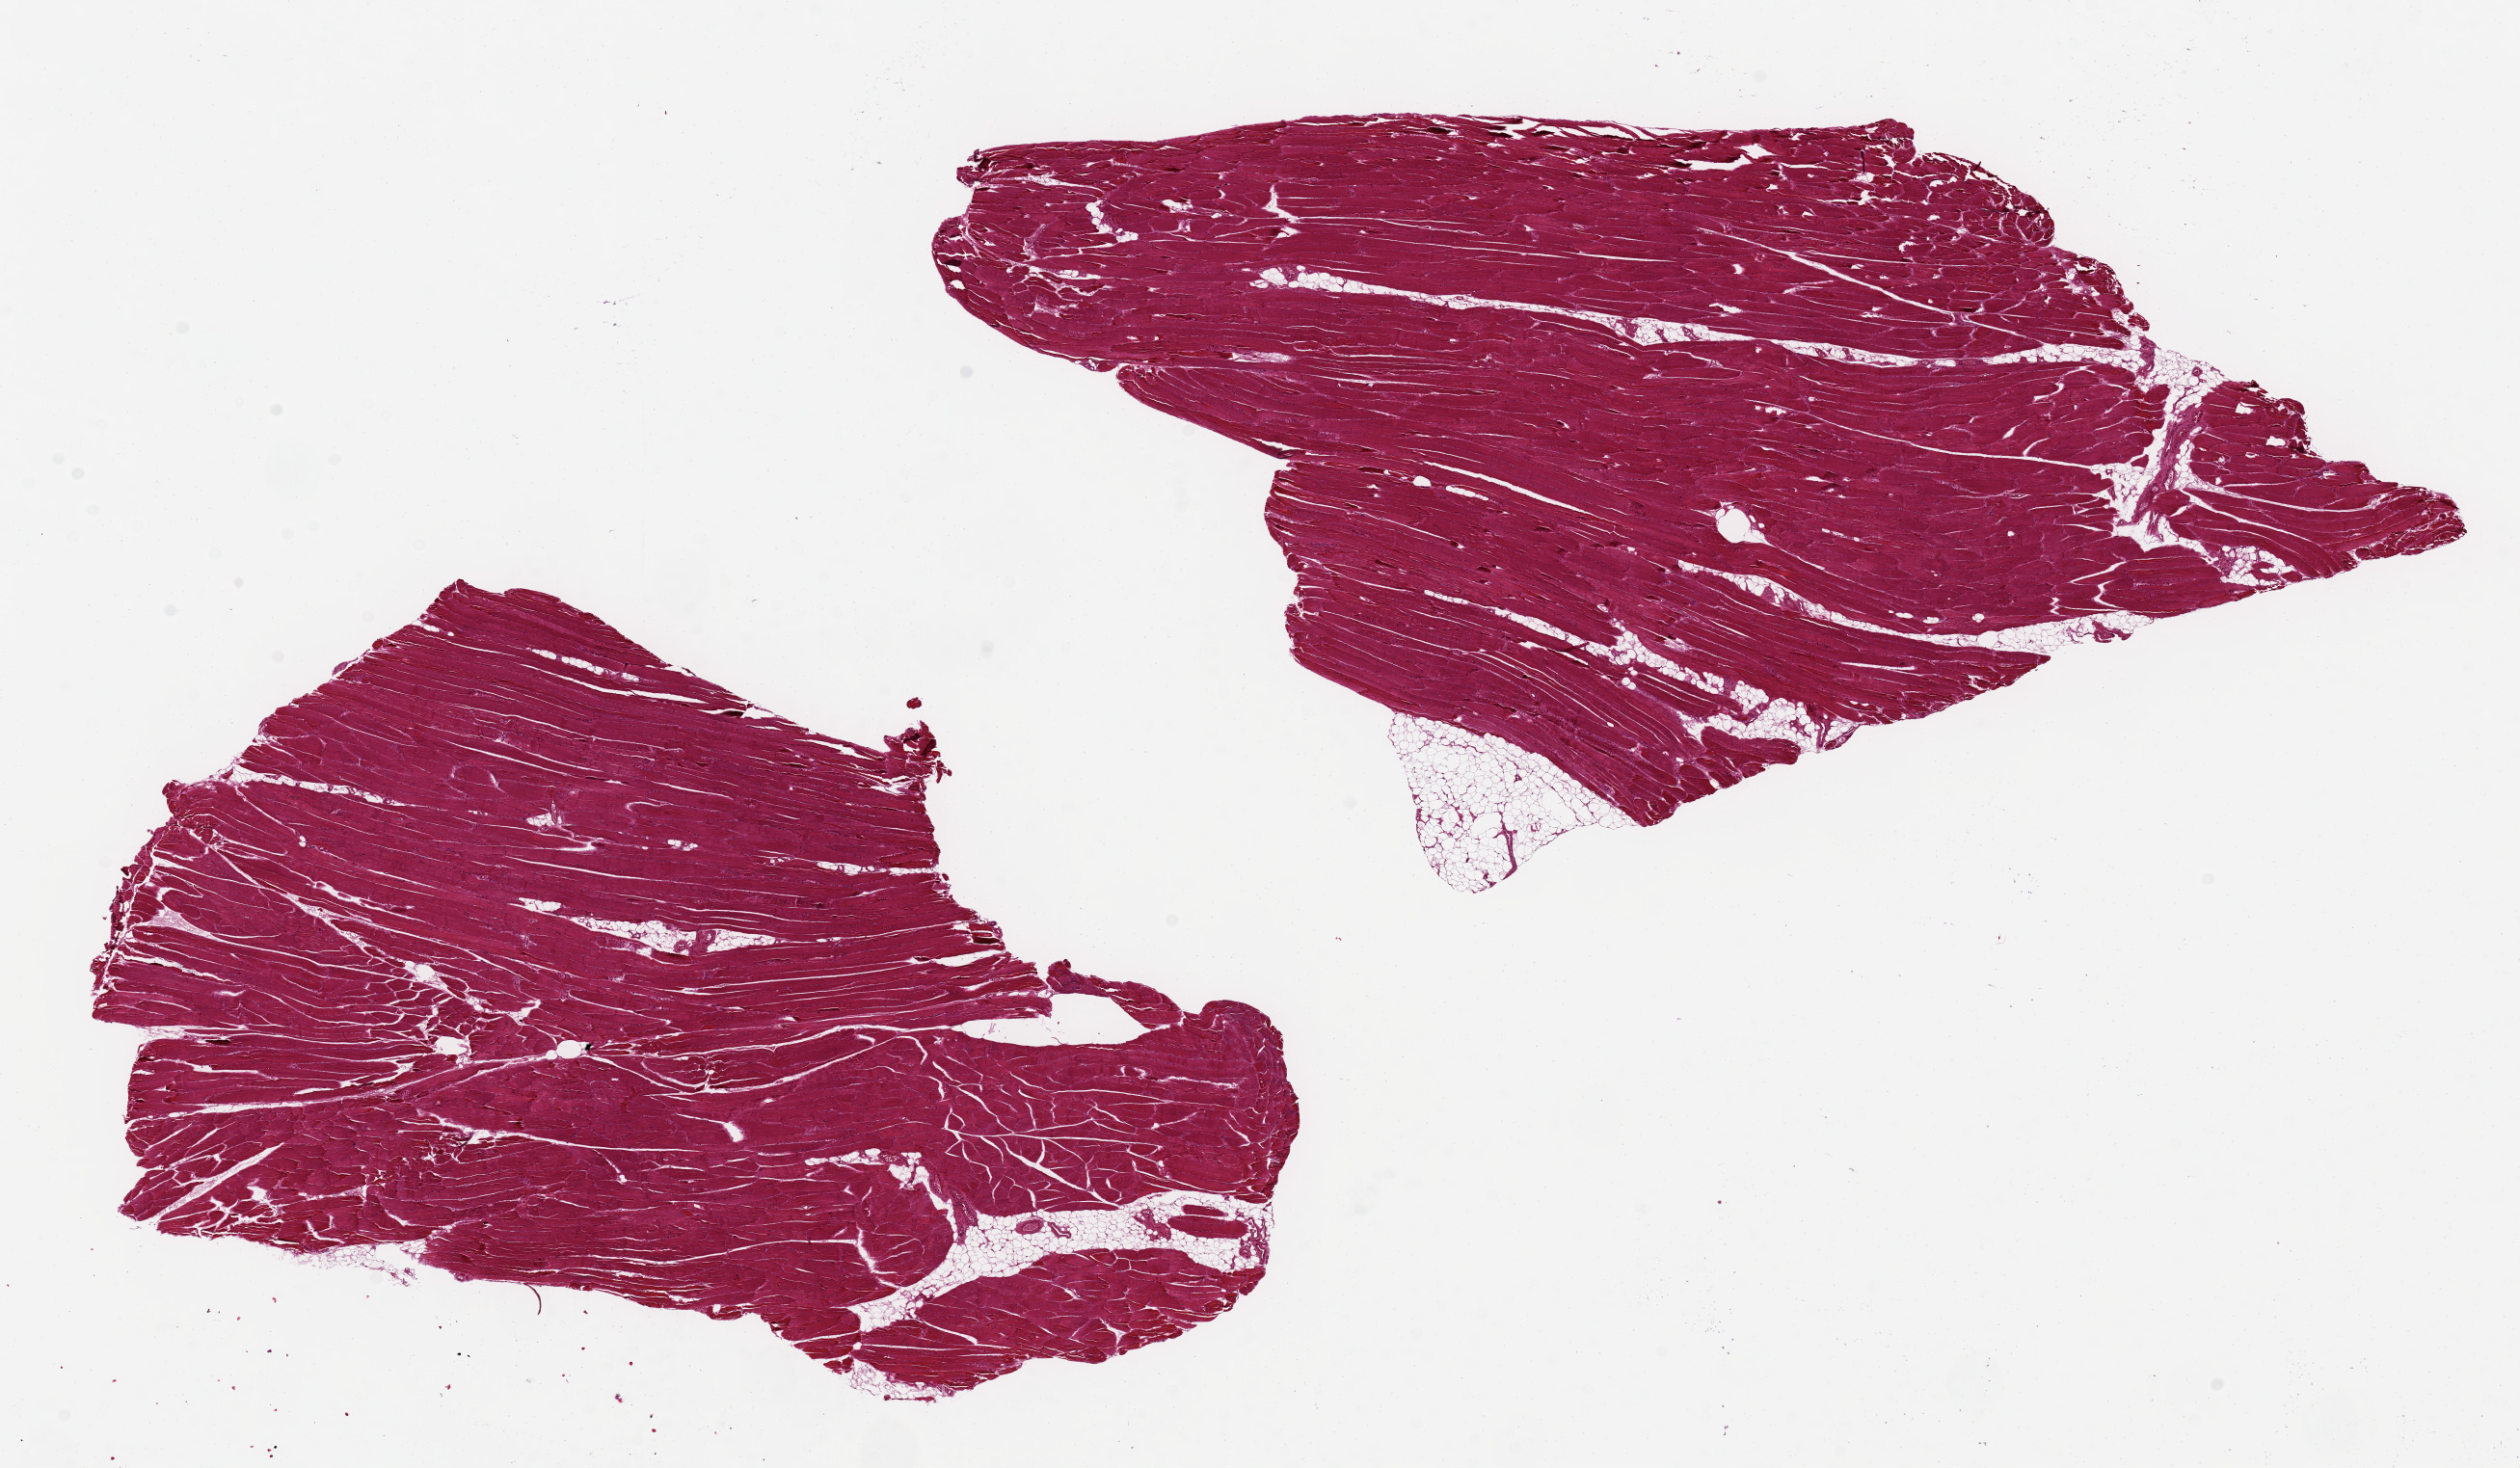
Digitized hematoxylin and eosin (H&E)-stained section, low-resolution overview of the scanned area, about 20.7 x 12.0 mm (slide scanned at 20x). PAXgene-fixed, paraffin-embedded tissue. Target tissue: skeletal muscle. Donor tissue sample. Donor: male.
Reviewer comment on this tissue sample: 2 aliquots, ~10x5mm, minimal interstitial fat.